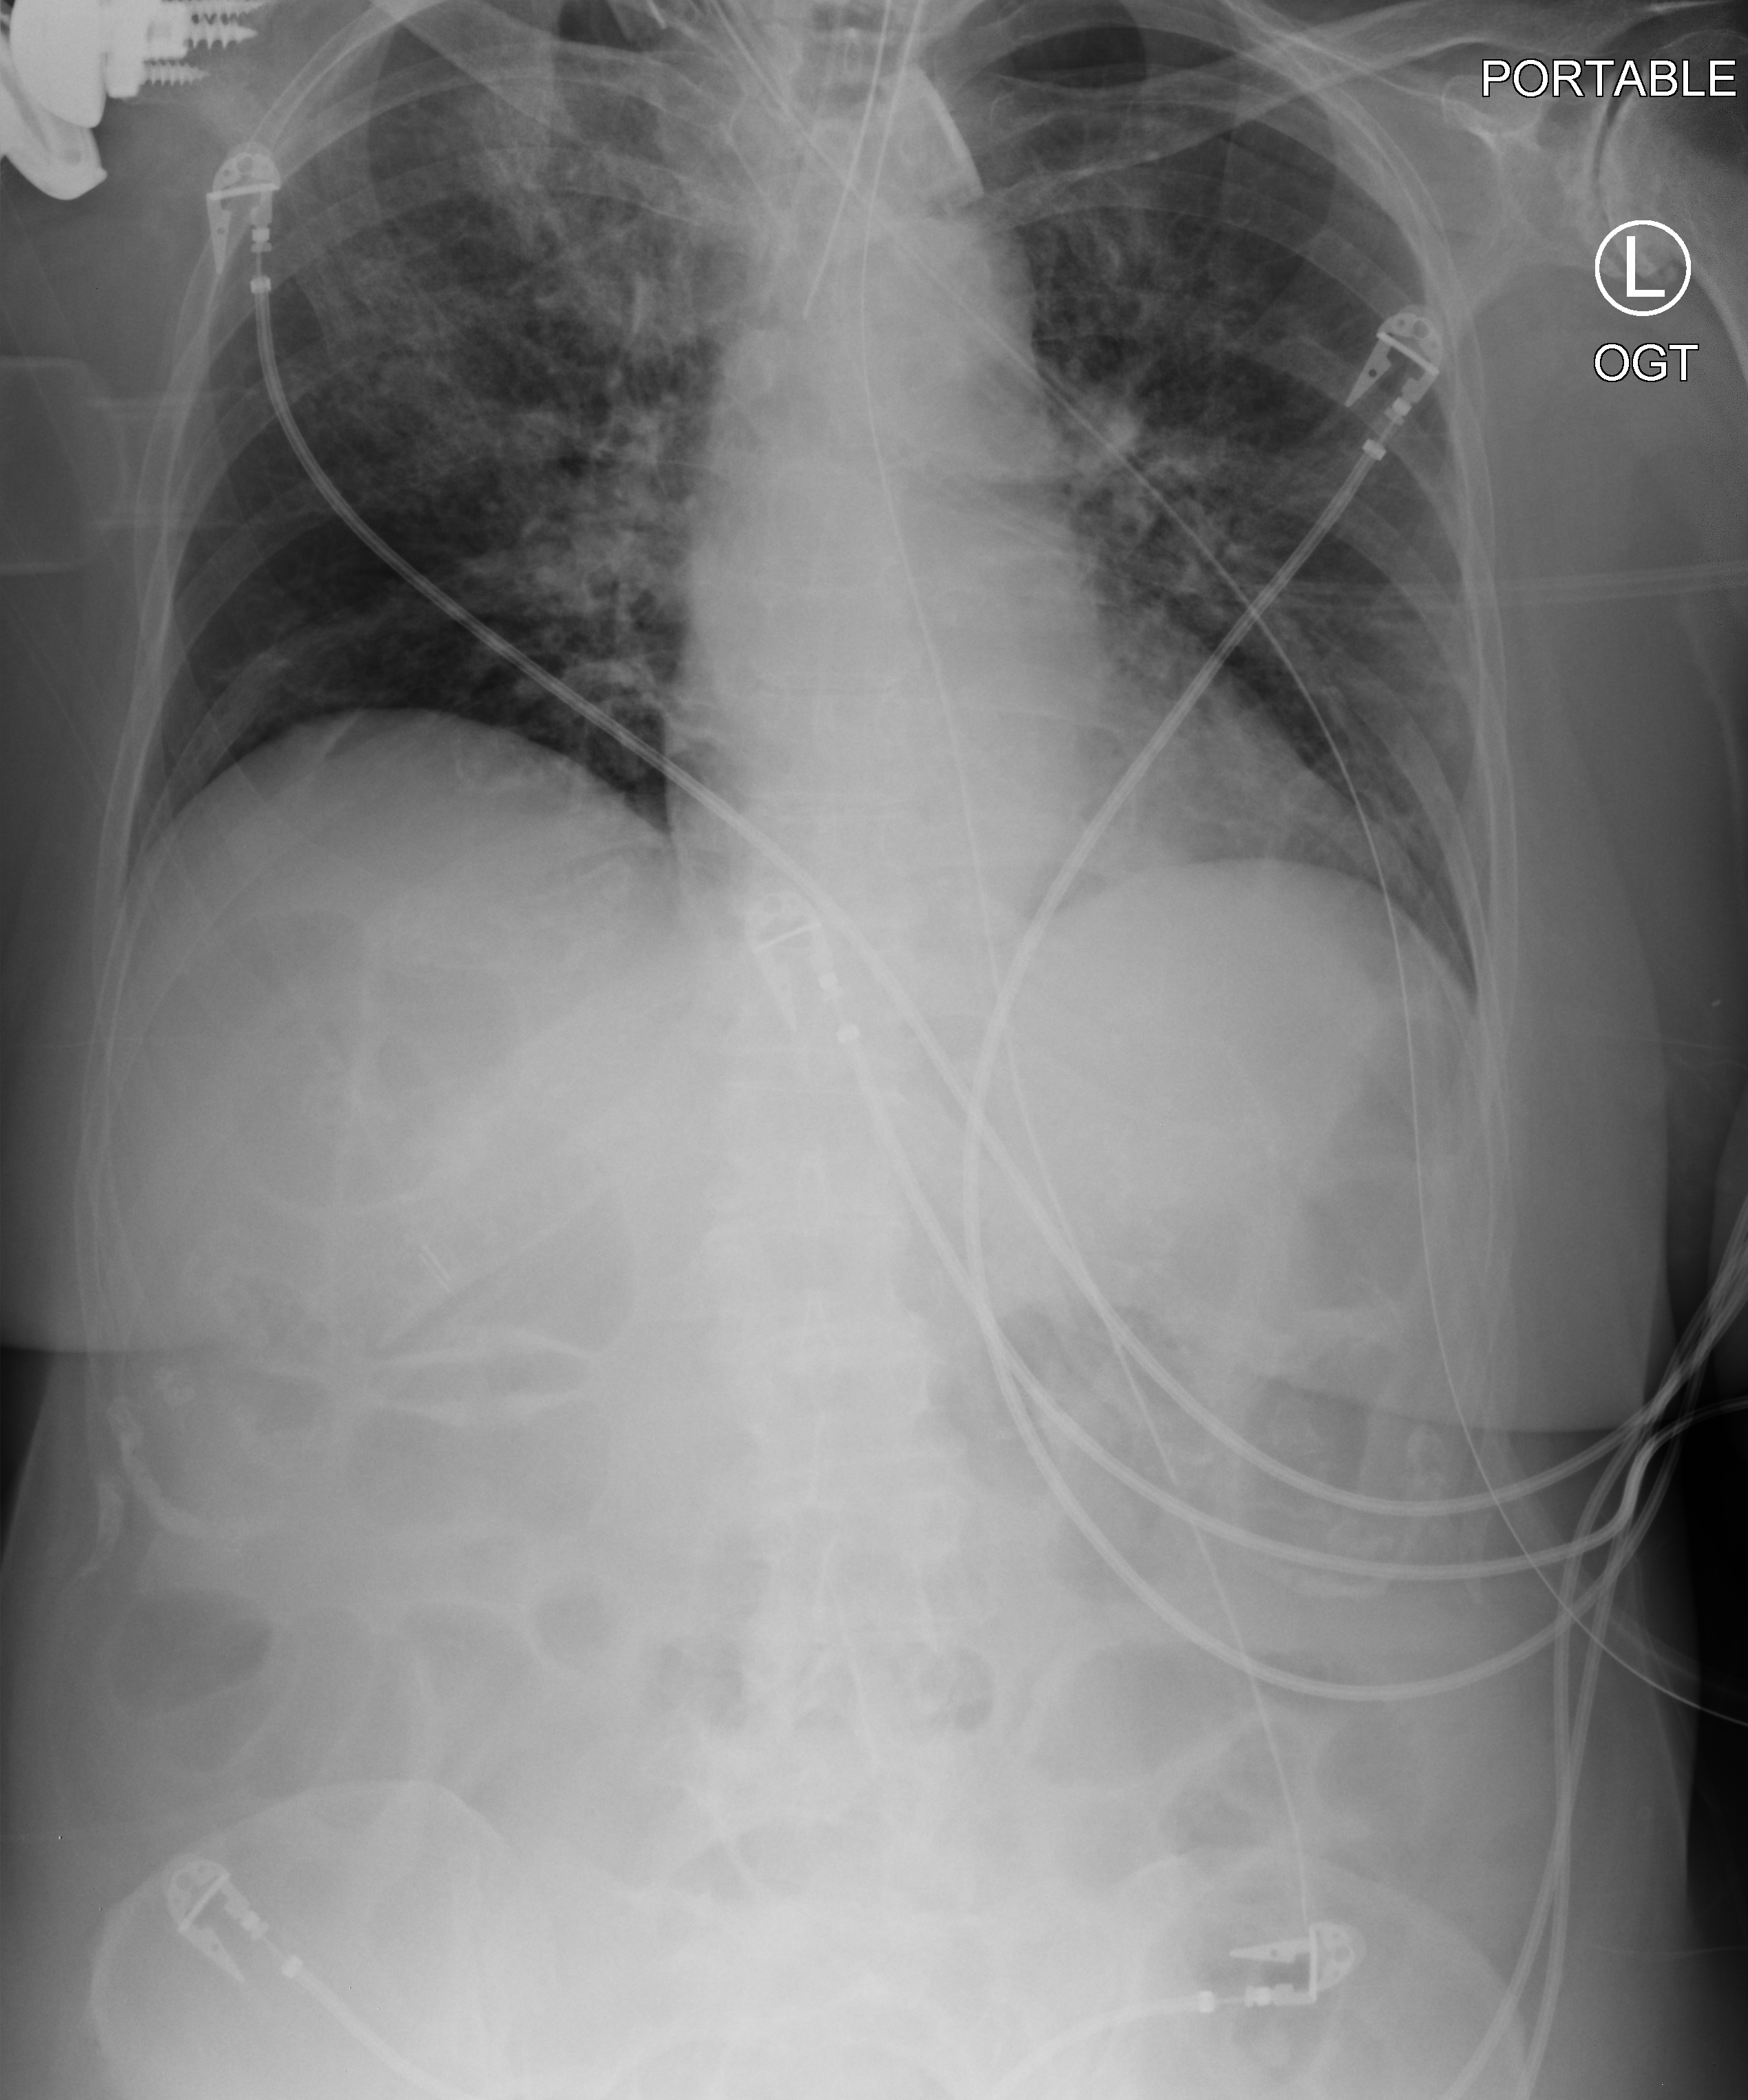
Portable chest radiograph. Female patient hospitalised with COVID-19, age 60–74 years.
Hospital-stay facts (about this admission, not read from this image; timing relative to this image not recorded):
- admitted to intensive care during this hospital stay: yes